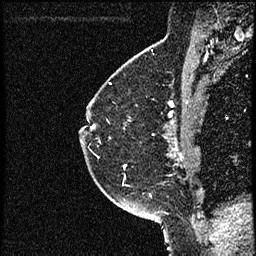
Breast MRI (dynamic contrast-enhanced), one sagittal slice. Position 40 of 52 along the scan axis. Dynamic contrast-enhanced study with each time point stored as its own series, time point 2 of 3 at this slice position (early post-contrast, ordered by acquisition time). 1.5 T. TE 4.2 ms, TR 17.6 ms. 2 mm slice thickness. 256 × 256 image matrix. Female patient, age 49 years. From the clinical record (not read from this slice): setting: breast cancer imaged before/during neoadjuvant chemotherapy; receptor status: HER2-positive.
Structures marked on this image (semi-automatic segmentation, software-assisted and operator-edited):
- analysis volume of interest (the breast-tissue region the enhancement analysis was run in; not a lesion): bounding box (x1, y1, x2, y2) in pixels: (85, 65, 182, 175)
- tumour enhancement mask (voxels above the 100 % enhancement threshold inside the analysis volume of interest): (172, 103, 182, 157)